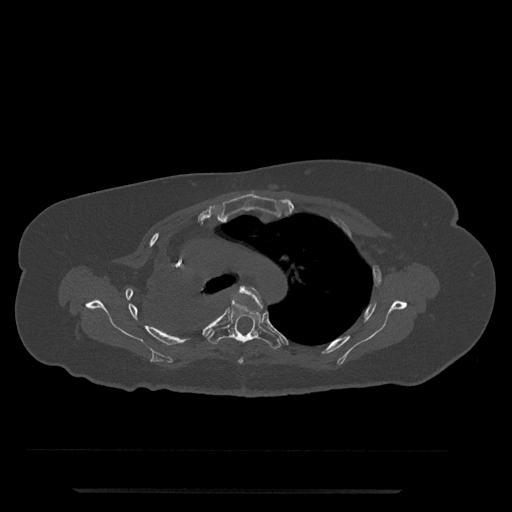
CT including the spine, one axial slice. Slice 556 of 797 in the series (ordered by position). Reconstruction kernel Br40s/3. 120 kVp. Bone window (W 1800 / L 400 HU). 0.5 mm slice thickness. 512 × 512 image matrix, field of view 440 × 440 mm. Female patient, age 51 years. From the clinical record (not read from this slice): primary cancer: neuro; vertebrae with lytic lesions (as recorded): T8.
Structures marked on this image (semi-automatic segmentation, software-assisted and operator-edited):
- T4 vertebra: bounding box (x1, y1, x2, y2) in pixels: (238, 286, 263, 364)
- T5 vertebra: (207, 298, 281, 349)